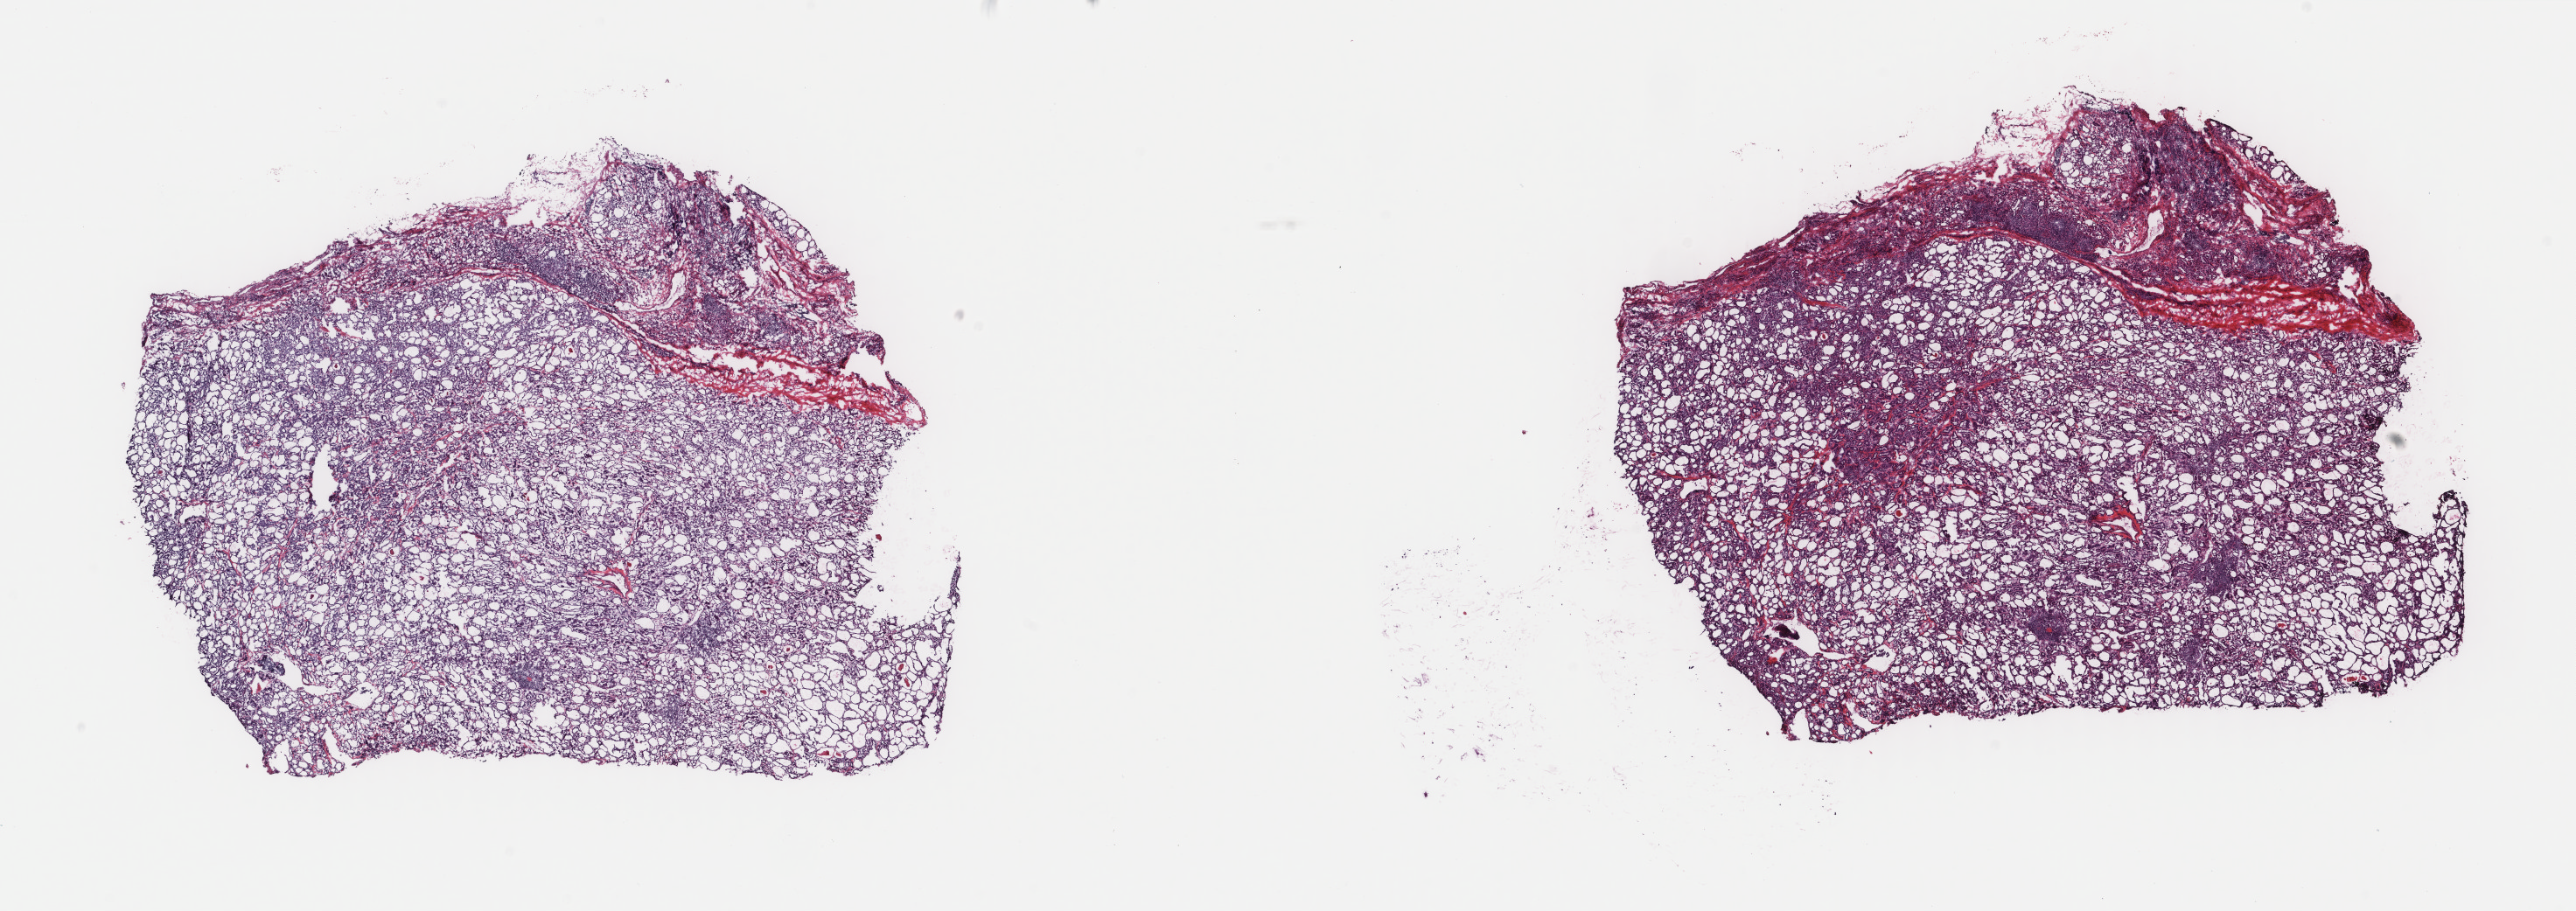
H&E-stained whole-slide image — whole scanned area (about 23.4 x 8.3 mm) shown as a low-resolution overview. Frozen section from the top of the tissue portion. Sample: primary tumour, thyroid. Female patient; age at initial diagnosis 54 years. Slide review estimates, as recorded: tumour cells 85%, tumour nuclei 85%.
Diagnosis: Papillary carcinoma, follicular variant (thyroid gland).